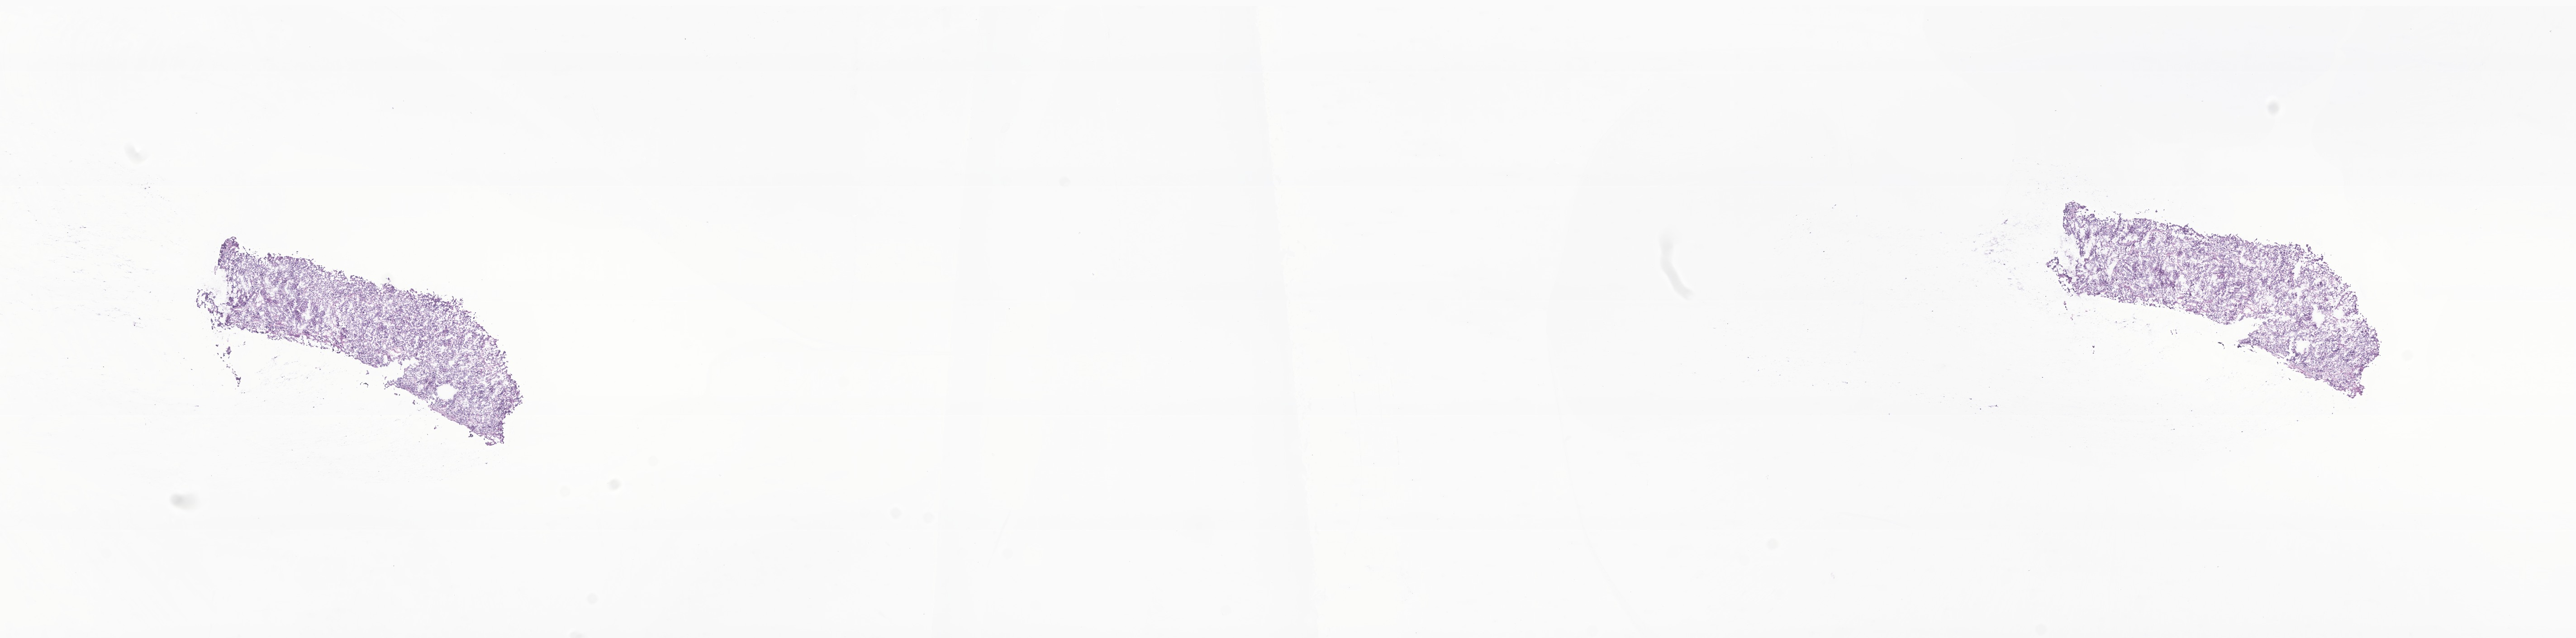
Digitized haematoxylin and eosin-stained section of tumor tissue from the abdomen, a low-resolution overview of the entire scanned area, about 24.0 x 5.9 mm; cryosection (OCT / tissue freezing medium). Patient female; age 501 days (about 1.4 years).
Diagnosis (ICD-O-3 morphology term): Neuroblastoma, NOS.